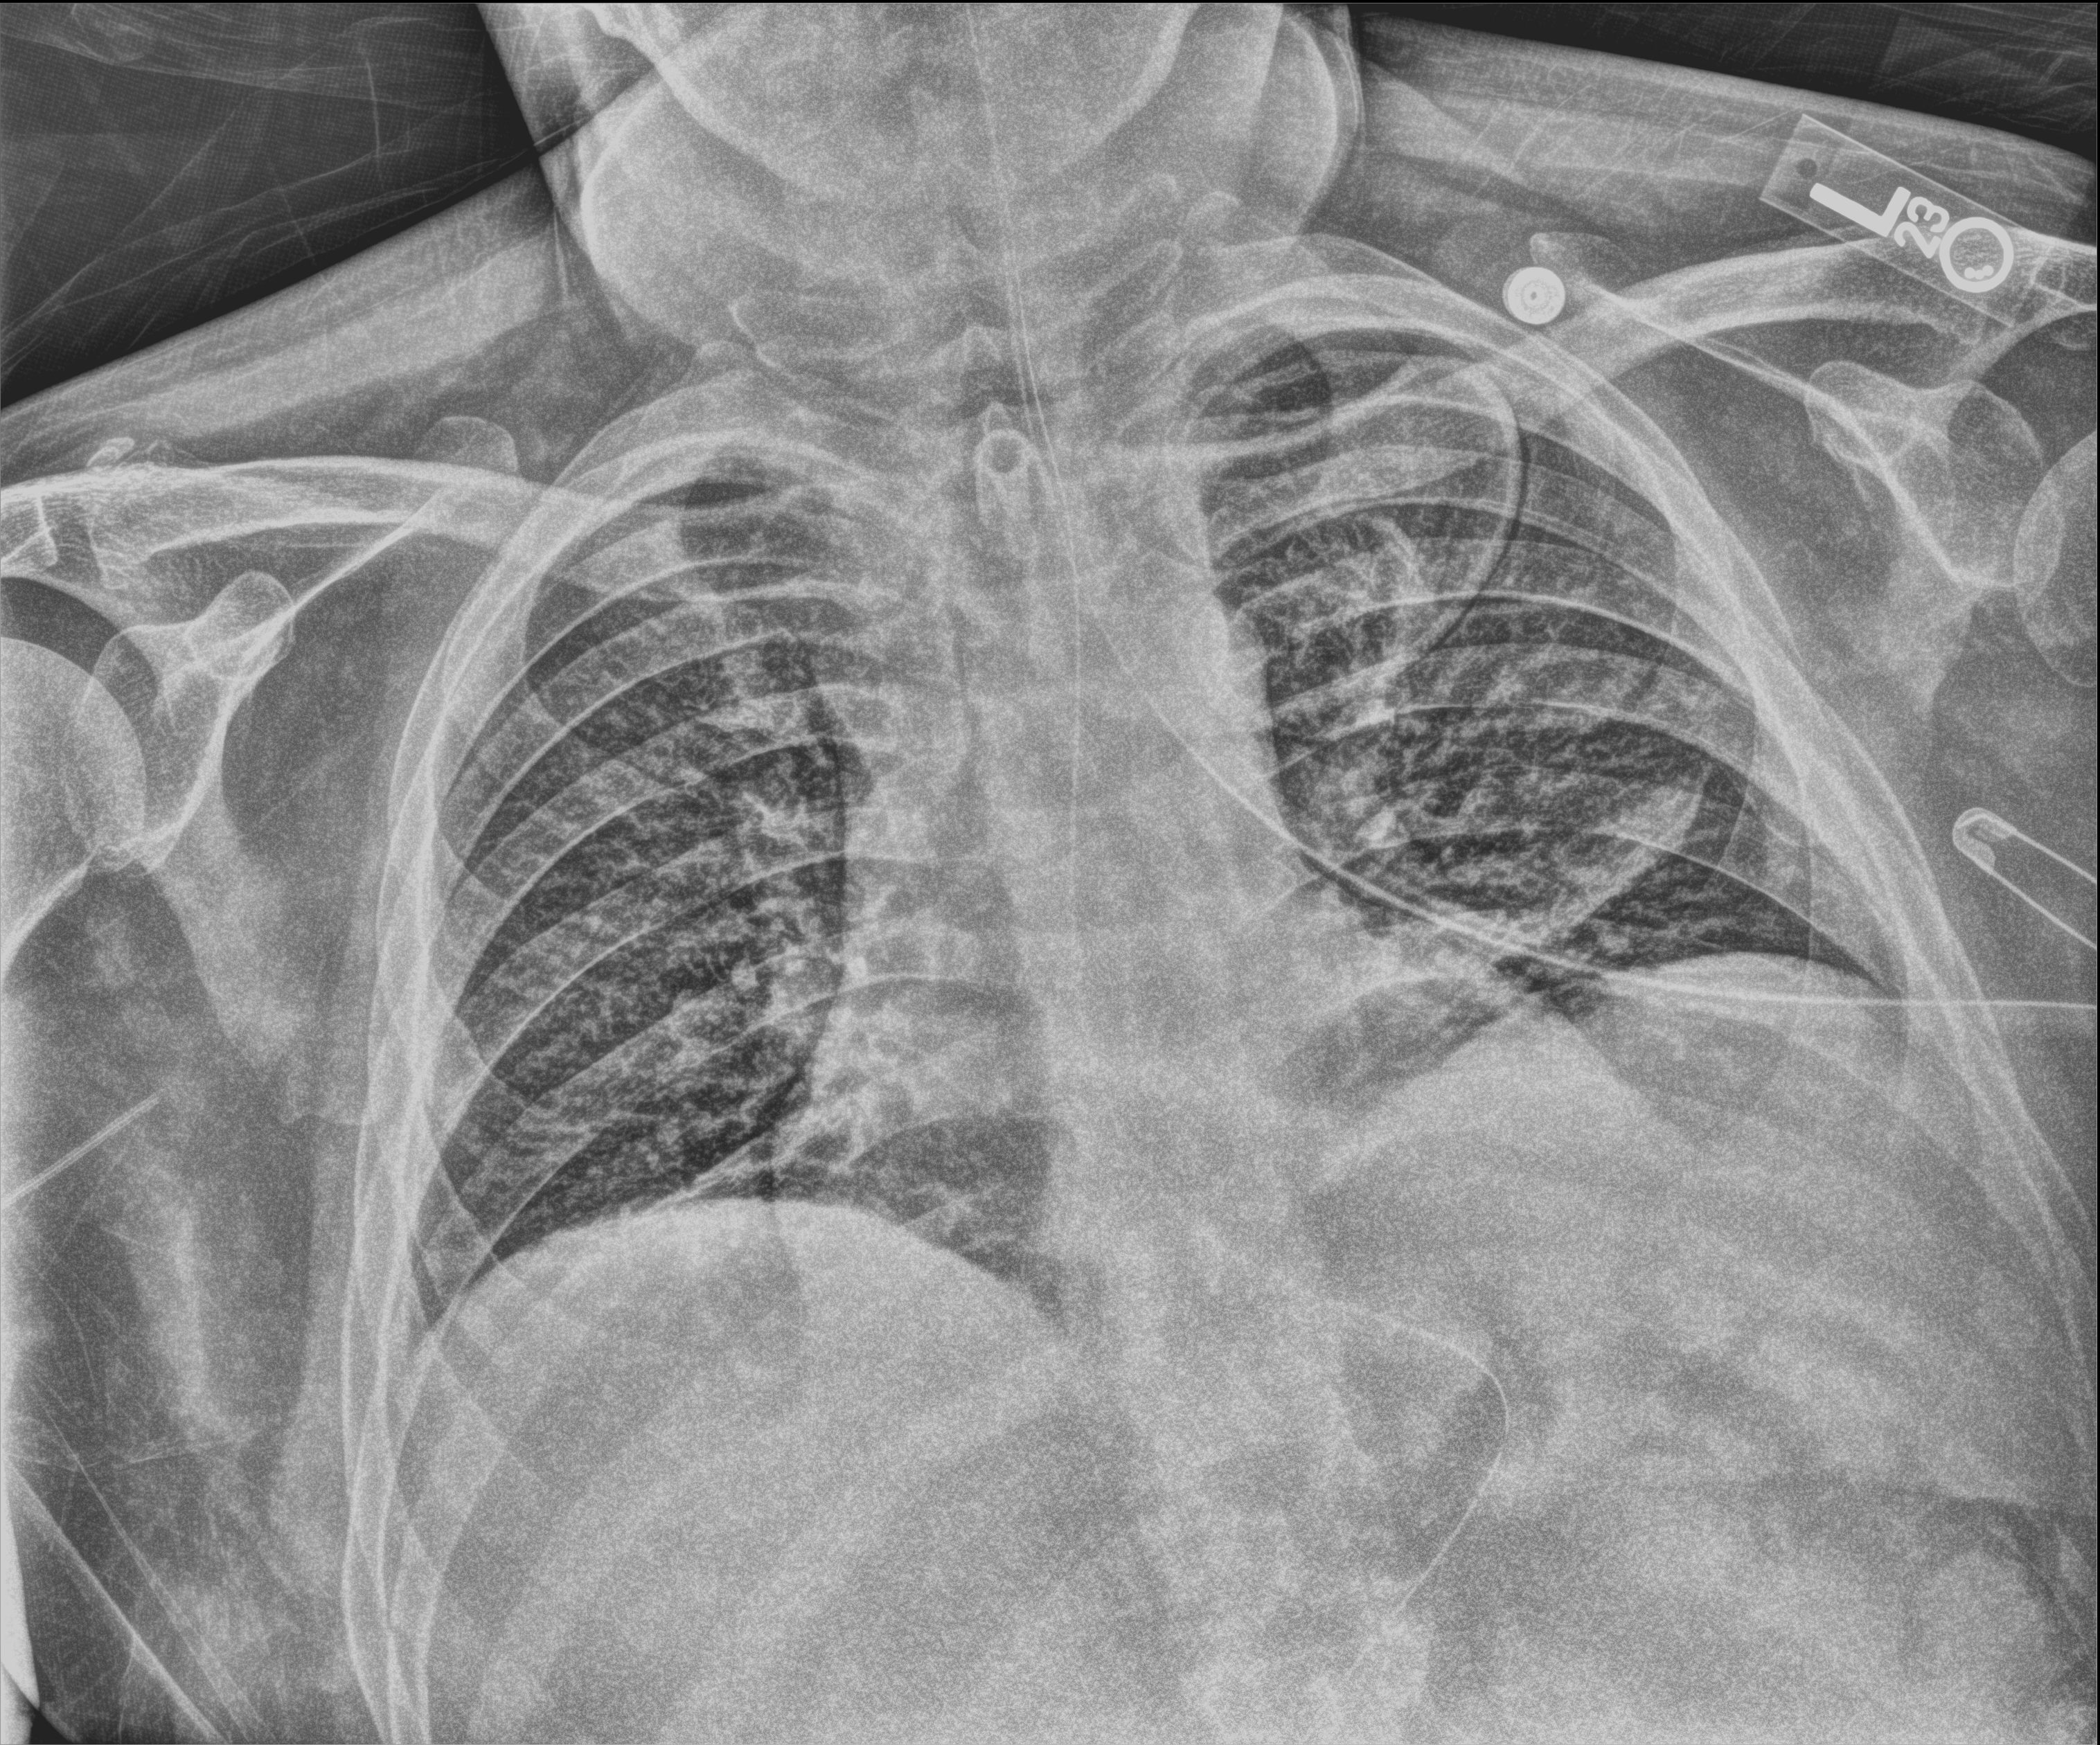
Chest X-ray (portable), anteroposterior (AP) projection. Male patient hospitalised with COVID-19, age 18–59 years.
Hospital-stay facts (about this admission, not read from this image; timing relative to this image not recorded): admitted to intensive care during this hospital stay: yes.